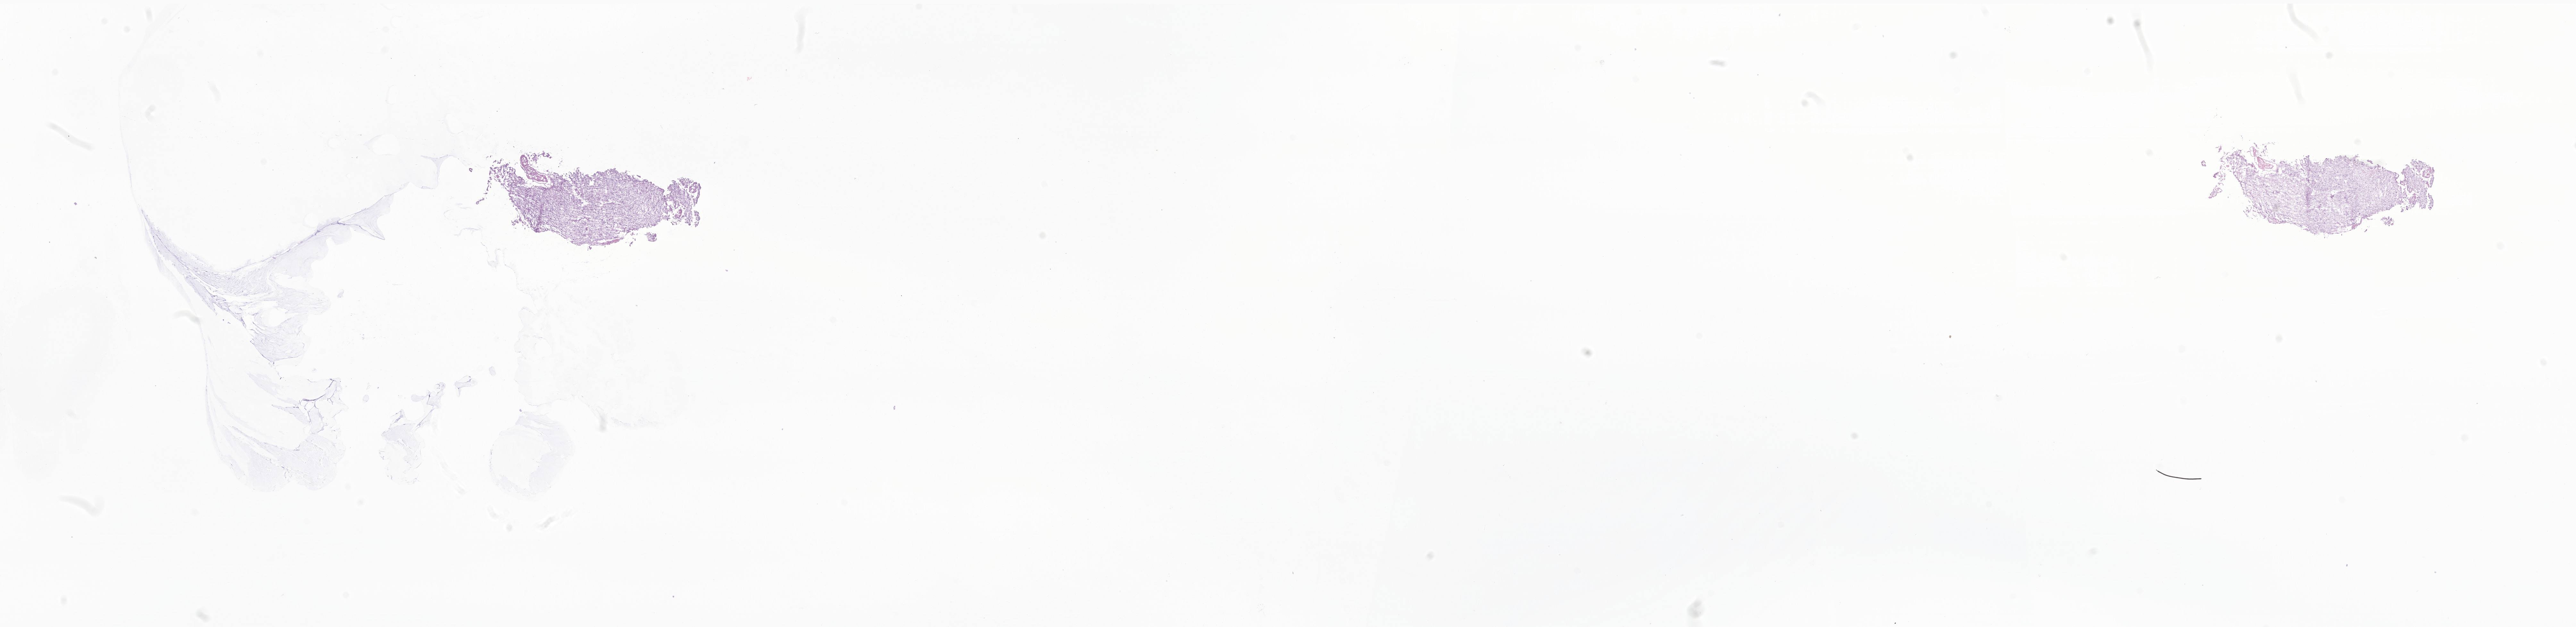
Digitized haematoxylin and eosin-stained section of tumor tissue from the brain — shown as a low-resolution overview of the whole scanned area (about 33.9 x 8.2 mm); frozen section (OCT-embedded). Female patient, age 164 months (13 years 8 months).
- diagnosis: Neoplasm, uncertain whether benign or malignant